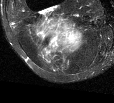
MRI of an extremity soft-tissue mass, one axial slice. Slice 34 of 44 in the series (ordered by position). T2-weighted fat-saturated. MR volume resampled by the dataset authors to the PET/CT grid (not the native acquisition matrix). 3.27 mm slice thickness. 114 × 103 image matrix, field of view 111 × 101 mm. Female patient. From the clinical record (not read from this slice): histological type: liposarcoma; site of the primary tumour: right thigh.
Structures marked on this image (expert contour drawn on MRI and transferred to this co-registered scan by the dataset authors):
- gross tumour volume (mass): bounding box (x1, y1, x2, y2) in pixels: (31, 16, 85, 56)